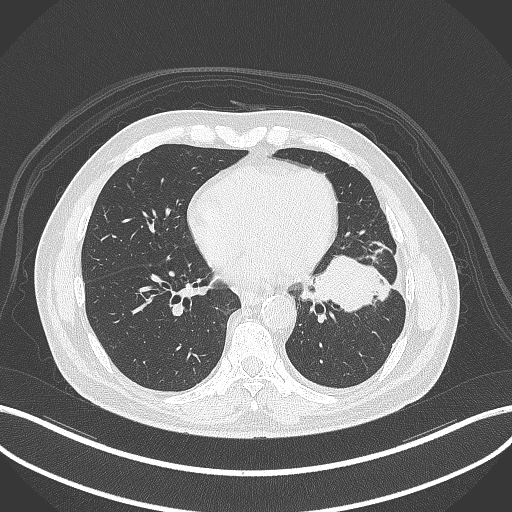
Chest CT, one axial slice. Slice 142 of 230 in the series (ordered by position). Reconstruction kernel B70f. Lung window (W 1500 / L -600 HU). 512 × 512 image matrix, field of view 400 × 400 mm. Male patient, age 68 years. From the clinical record (not read from this slice): clinical TNM (as recorded): T2b N0 M0.
Outlined on this slice (rectangle marked by the reading radiologist):
- lung tumour (recorded histology: squamous cell carcinoma): bounding box (x1, y1, x2, y2) in pixels: (312, 249, 396, 312)